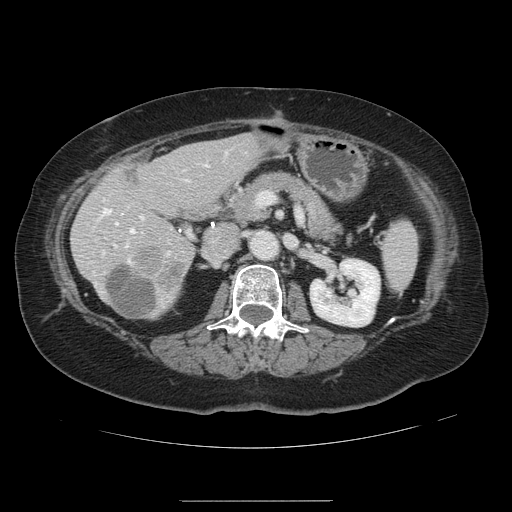
Contrast-enhanced abdominal CT, one axial slice; position 58 of 141 along the scan axis; 120 kVp; intravenous contrast given; soft-tissue window (W 400 / L 40 HU); 2.5 mm slice thickness; 512 × 512 image matrix. Female patient, age 74 years. From the clinical record (not read from this slice): diagnosis: colorectal cancer liver metastases, imaged before liver resection; multiple liver metastases: yes.
Outlined on this slice (expert manual segmentation):
- hepatic veins: bounding box (x1, y1, x2, y2) in pixels: (100, 208, 134, 262)
- liver: (72, 136, 262, 320)
- planned liver remnant (the part of the liver to remain after resection): (74, 136, 262, 318)
- portal vein (with intrahepatic branches): (114, 152, 226, 255)
- liver metastasis: (109, 266, 159, 317)
- liver metastasis: (132, 245, 188, 291)